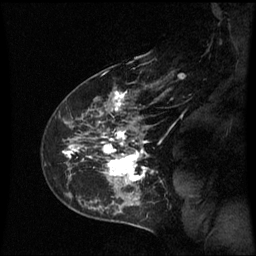
Breast MRI (dynamic contrast-enhanced), one sagittal slice. Dynamic contrast-enhanced series, image 2 of 3 at this slice position (ordered by acquisition). 1.5 T. TE 4.2 ms, TR 8.9 ms. 2.3 mm slice thickness. 256 × 256 image matrix. Patient: female, 43 years. Case-level facts recorded for this patient, not image findings: setting: breast cancer imaged before/during neoadjuvant chemotherapy; receptor status: HER2-positive.
Structures marked on this image (semi-automatic segmentation, software-assisted and operator-edited):
- analysis volume of interest (the breast-tissue region the enhancement analysis was run in; not a lesion): box from (x=56, y=80) to (x=162, y=195) px
- tumour enhancement mask (voxels above the 70 % enhancement threshold inside the analysis volume of interest): (x=63, y=91)–(x=149, y=183)